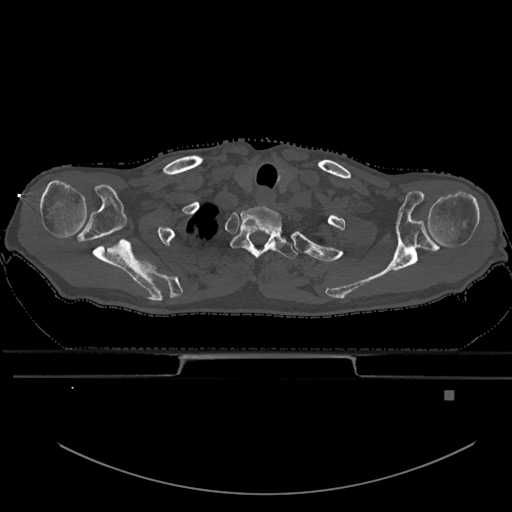
CT including the spine, one axial slice. Slice 545 of 969 in the series (ordered by position). Bone window (W 1800 / L 400 HU). 0.5 mm slice thickness. 512 × 512 image matrix, field of view 456 × 456 mm. Male patient, age 82 years. From the clinical record (not read from this slice): primary cancer: prostate; vertebrae with lytic lesions (as recorded): T11, T9, T8, T2.
Annotated regions visible in this slice (semi-automatic segmentation, software-assisted and operator-edited):
- T1 vertebra: bounding box [x1, y1, x2, y2] px = [231, 226, 298, 260]